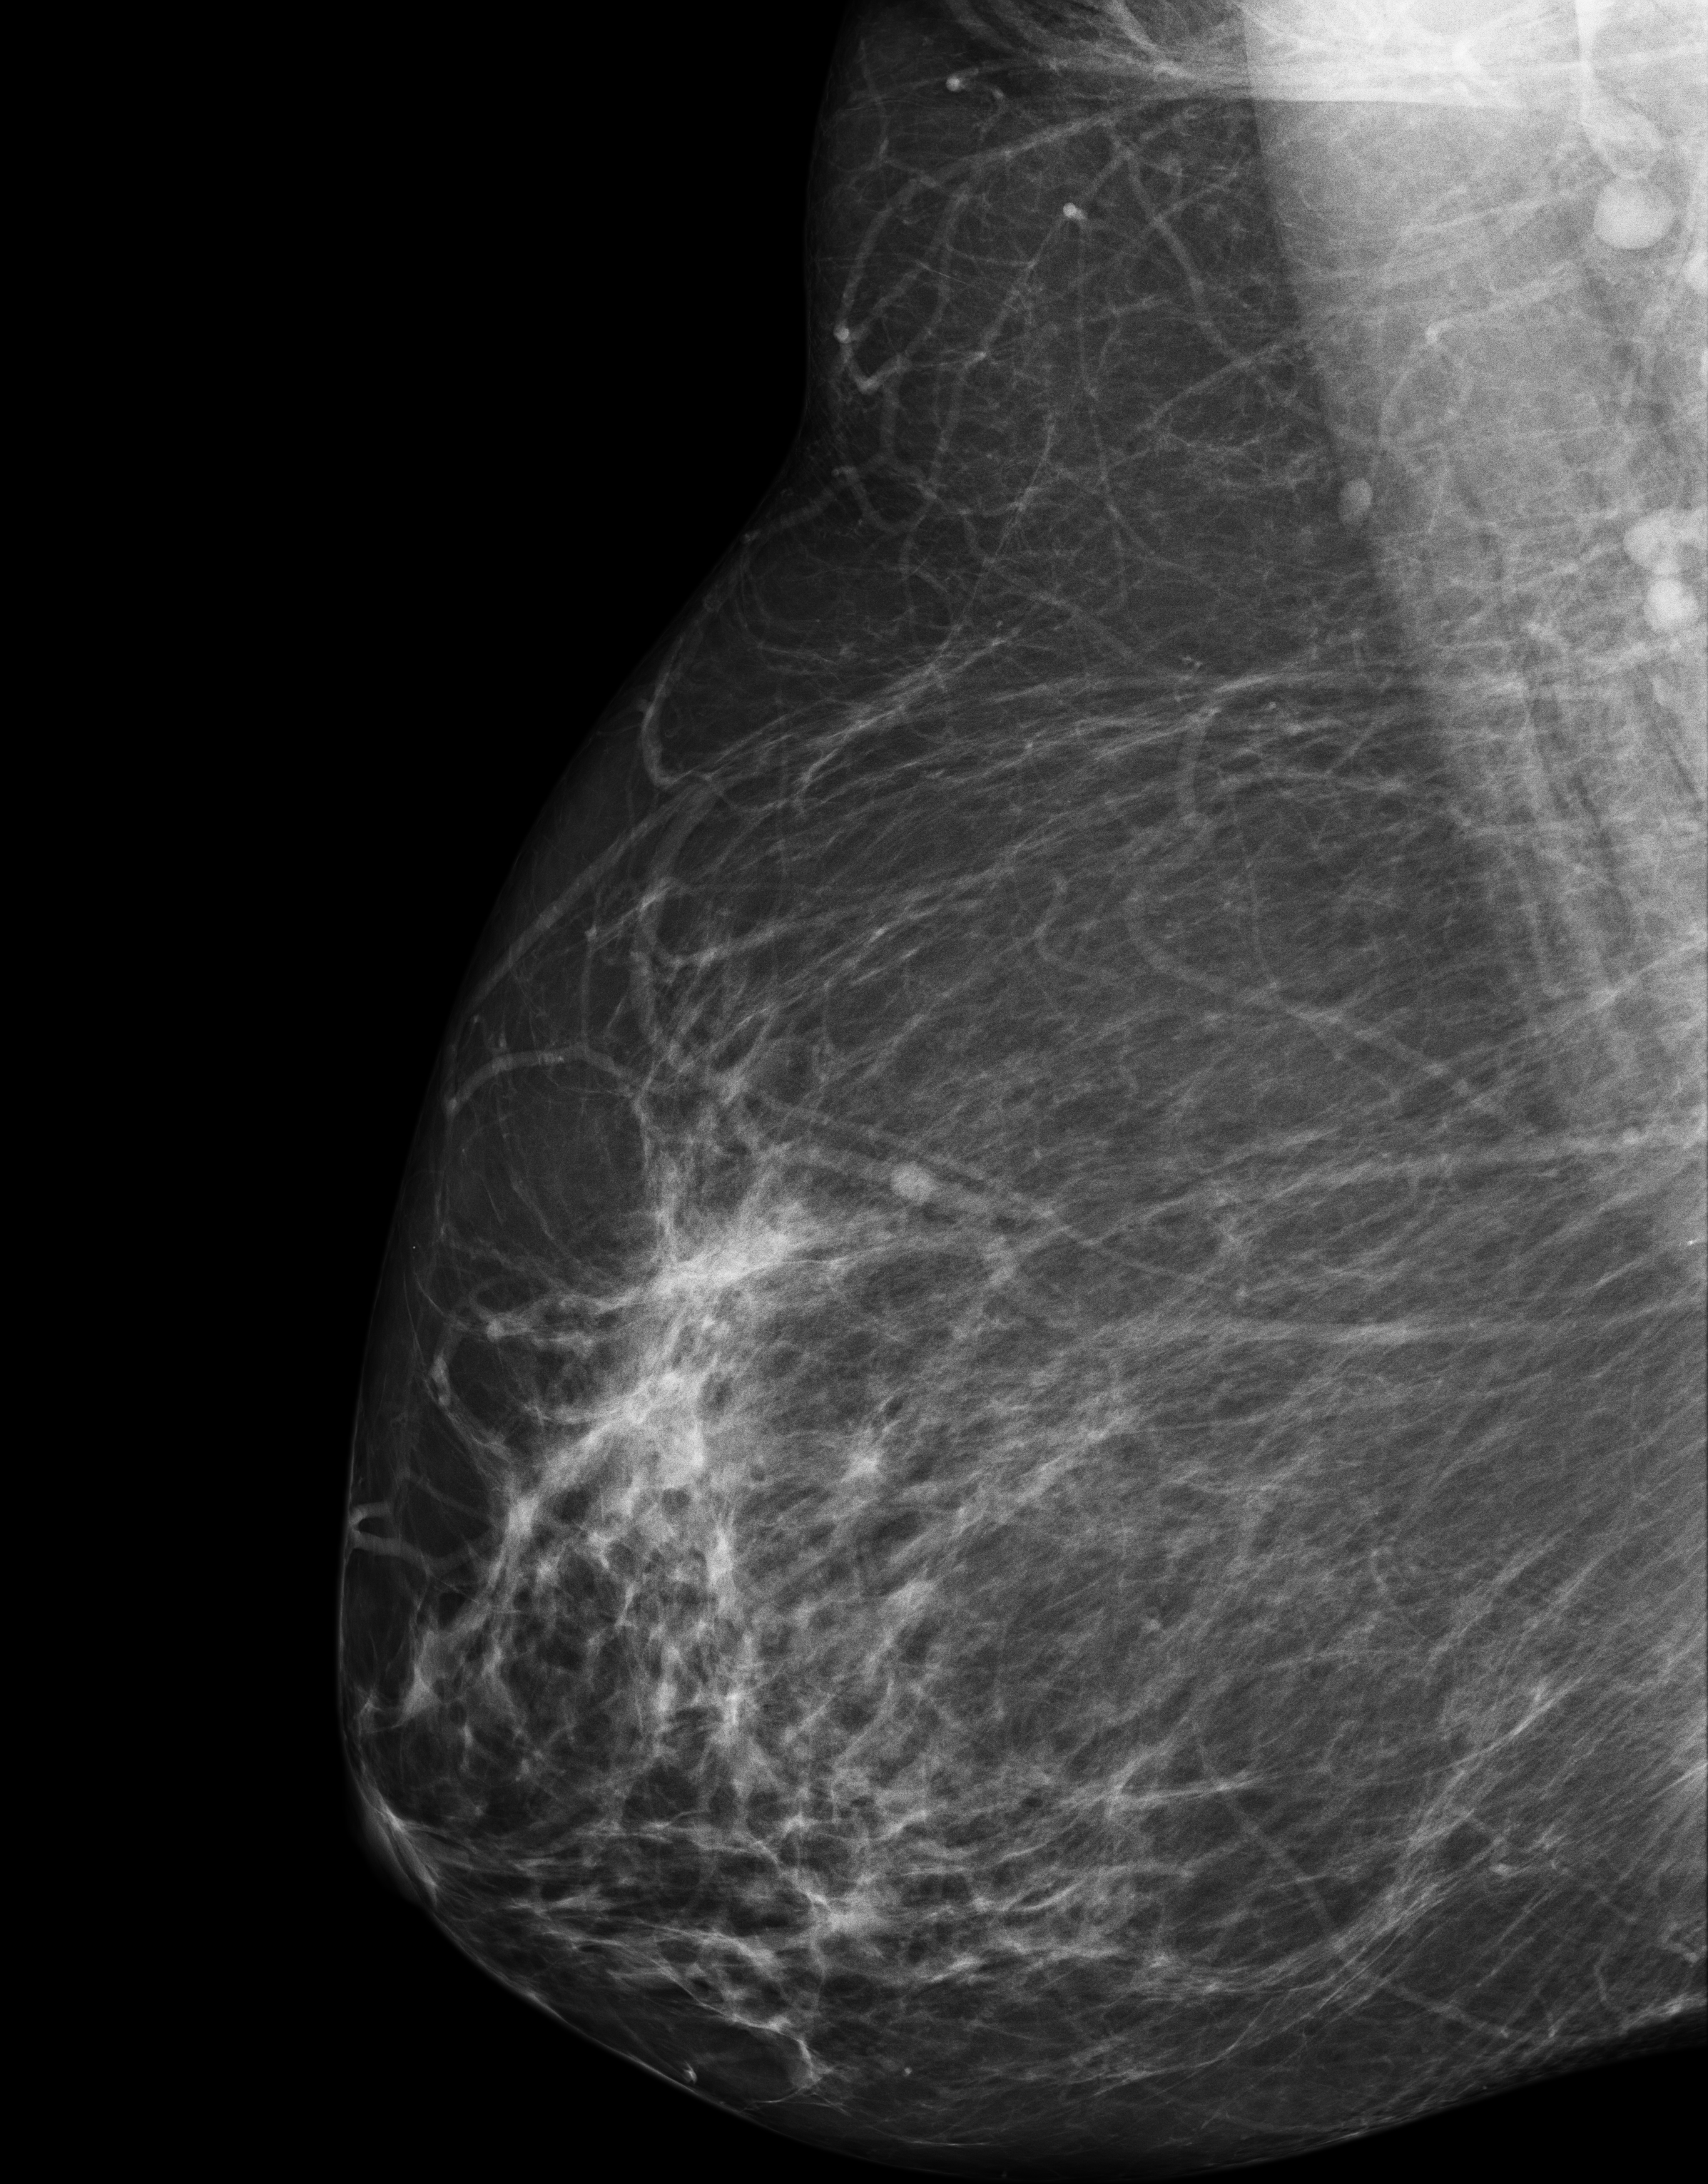
Screening examination, system: Senographe Essential ADS_56.21.3. Patient: female, 59 years.
Image type: full-field digital mammogram. Breast: right. Projection: medio-lateral oblique projection.